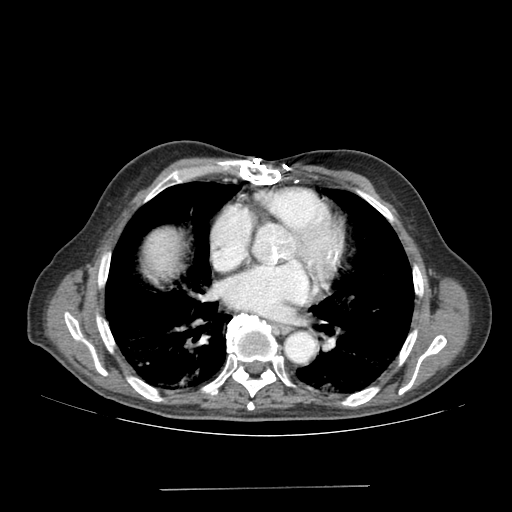
Contrast-enhanced abdominal CT (liver protocol), one axial slice; slice 180 of 192 in the series (ordered by position); reconstruction kernel SOFT; 120 kVp; soft-tissue window (W 400 / L 40 HU); 512 × 512 image matrix, field of view 400 × 400 mm. Case-level facts recorded for this patient, not image findings: diagnosis: hepatocellular carcinoma (patient treated with transarterial chemoembolisation; whether this scan precedes or follows treatment is not stated here); TNM stage (as recorded): Stage-IVA; Child-Pugh class: A; tumour differentiation: poorly differentiated.
Structures marked on this image (semi-automatic segmentation, software-assisted and operator-edited):
- liver parenchyma outside the tumour (the mass and vessels are separate outlines, so this box may not span the whole liver): bounding box [x1, y1, x2, y2] px = [144, 228, 178, 278]